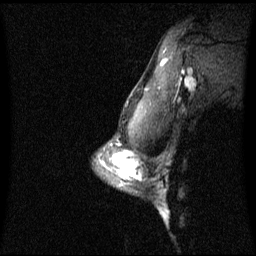
Breast MRI (dynamic contrast-enhanced), one sagittal slice. Slice 51 of 60 in the series (ordered by position). Dynamic contrast-enhanced series, image 2 of 3 at this slice position (ordered by acquisition). 1.5 T. TE 4.2 ms, TR 8.4 ms. 2.3 mm slice thickness. 256 × 256 image matrix, field of view 240 × 240 mm. Female patient, age 42 years. Case-level facts recorded for this patient, not image findings: setting: breast cancer imaged before/during neoadjuvant chemotherapy; receptor status: triple-negative.
Outlined on this slice (semi-automatically segmented with operator editing):
- analysis volume of interest (the breast-tissue region the enhancement analysis was run in; not a lesion): box from (x=106, y=156) to (x=138, y=189) px
- tumour enhancement mask (voxels above the 70 % enhancement threshold inside the analysis volume of interest): (x=113, y=156)–(x=136, y=177)